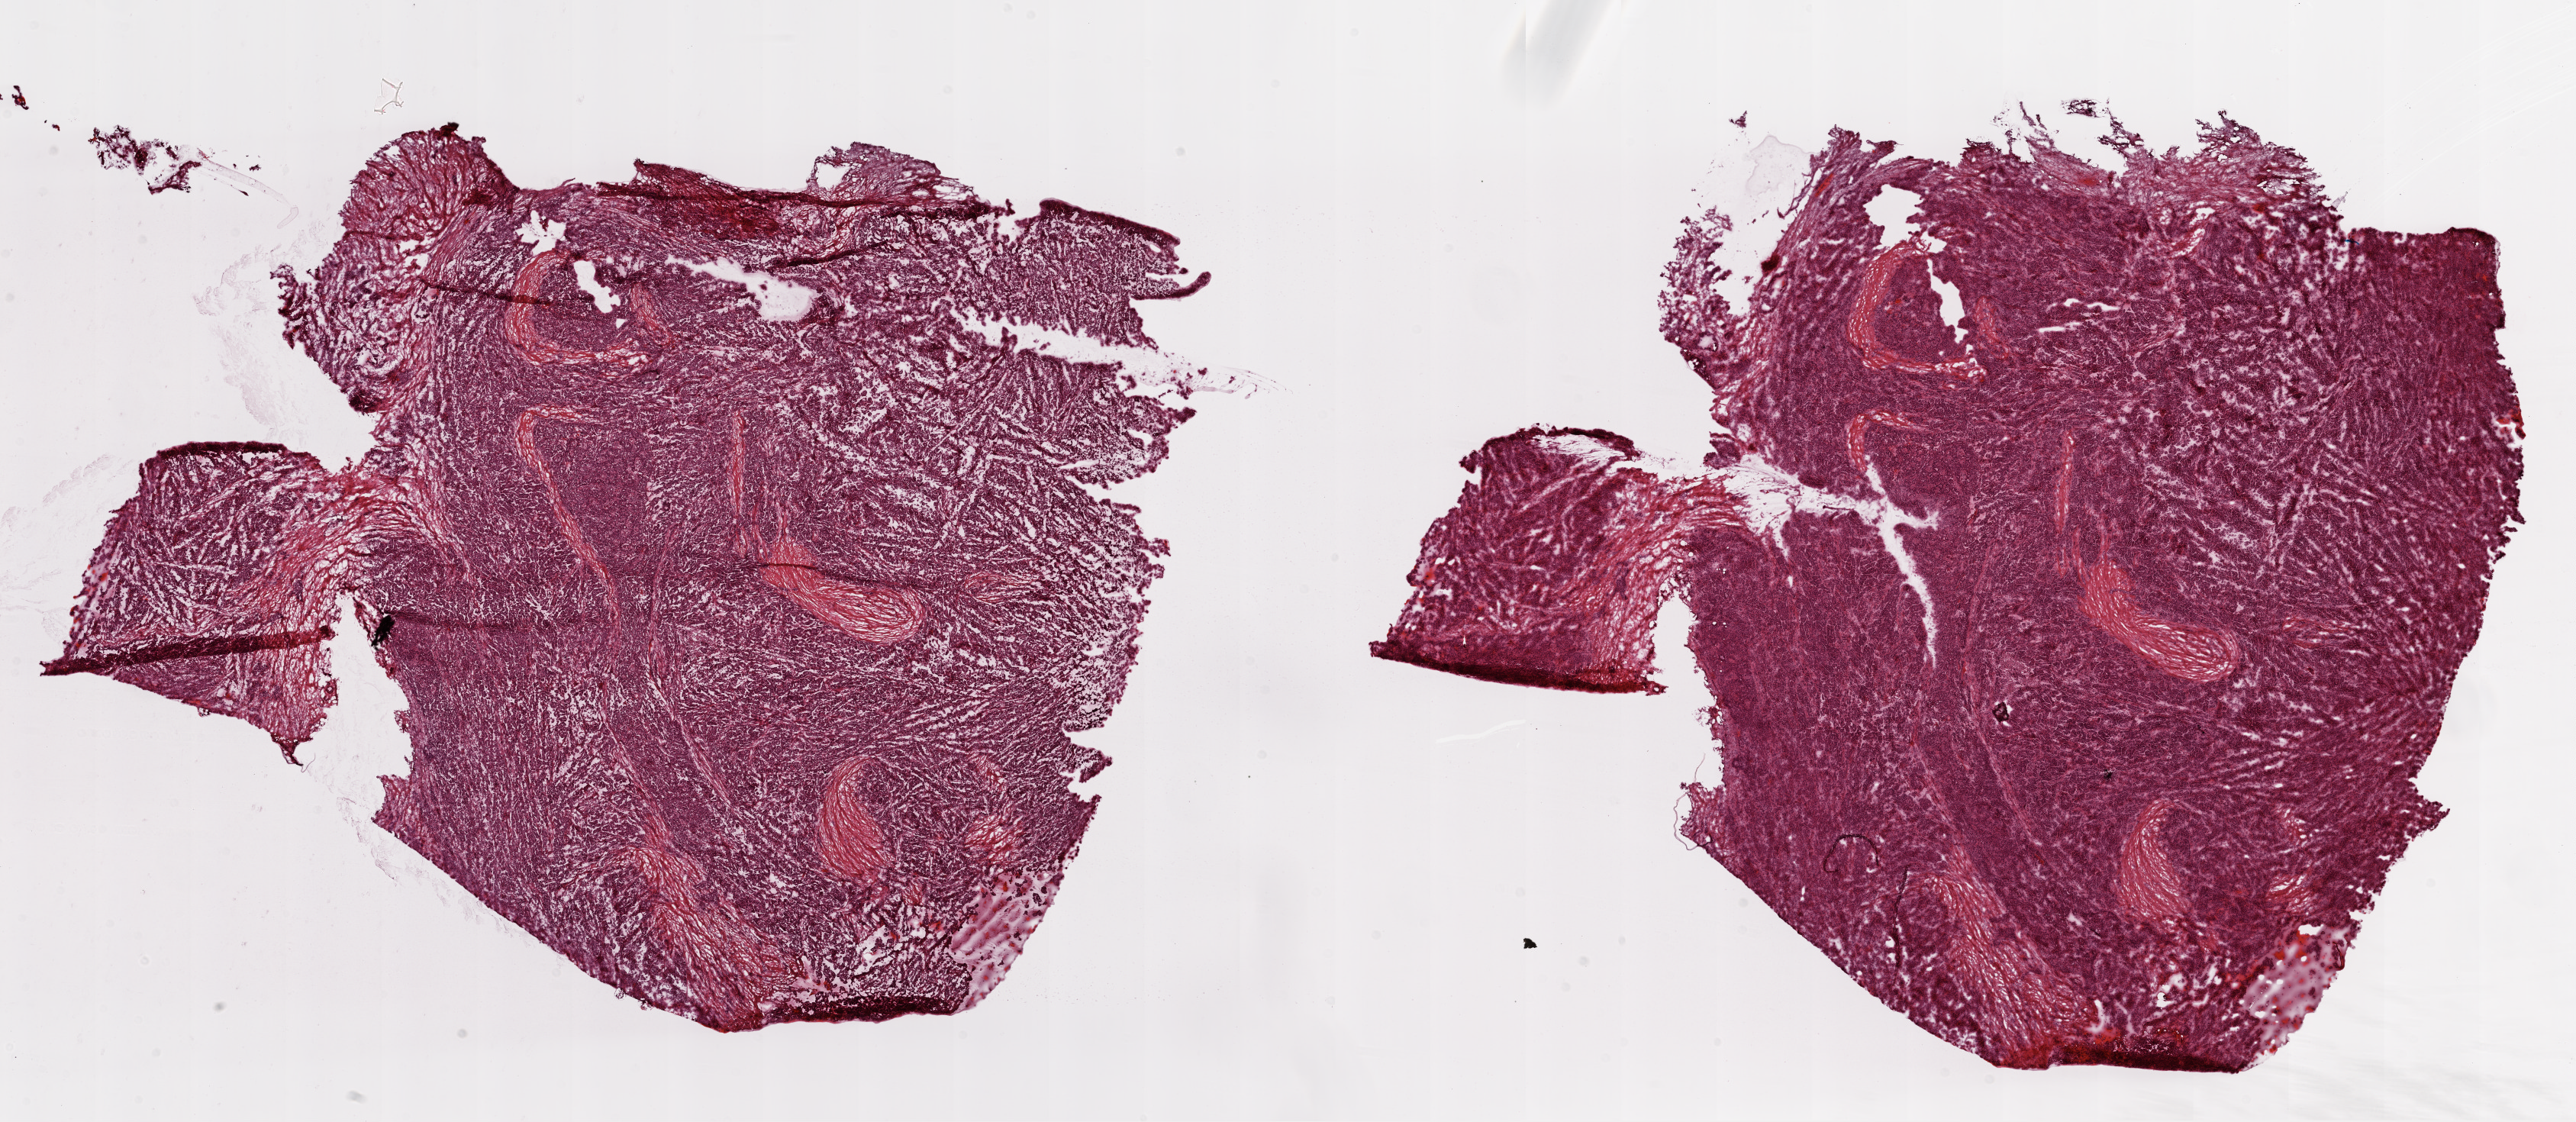
Whole-slide histology image, H&E-stained — whole scanned area (about 27.1 x 11.8 mm) shown as a low-resolution overview. Frozen section. Primary tumour sample from the ovary. Female patient; age at initial diagnosis 53 years. Pathologist review of this section (percent, as recorded): tumour cells 90%, tumour nuclei 90%.
Histologic diagnosis: Serous cystadenocarcinoma, NOS.